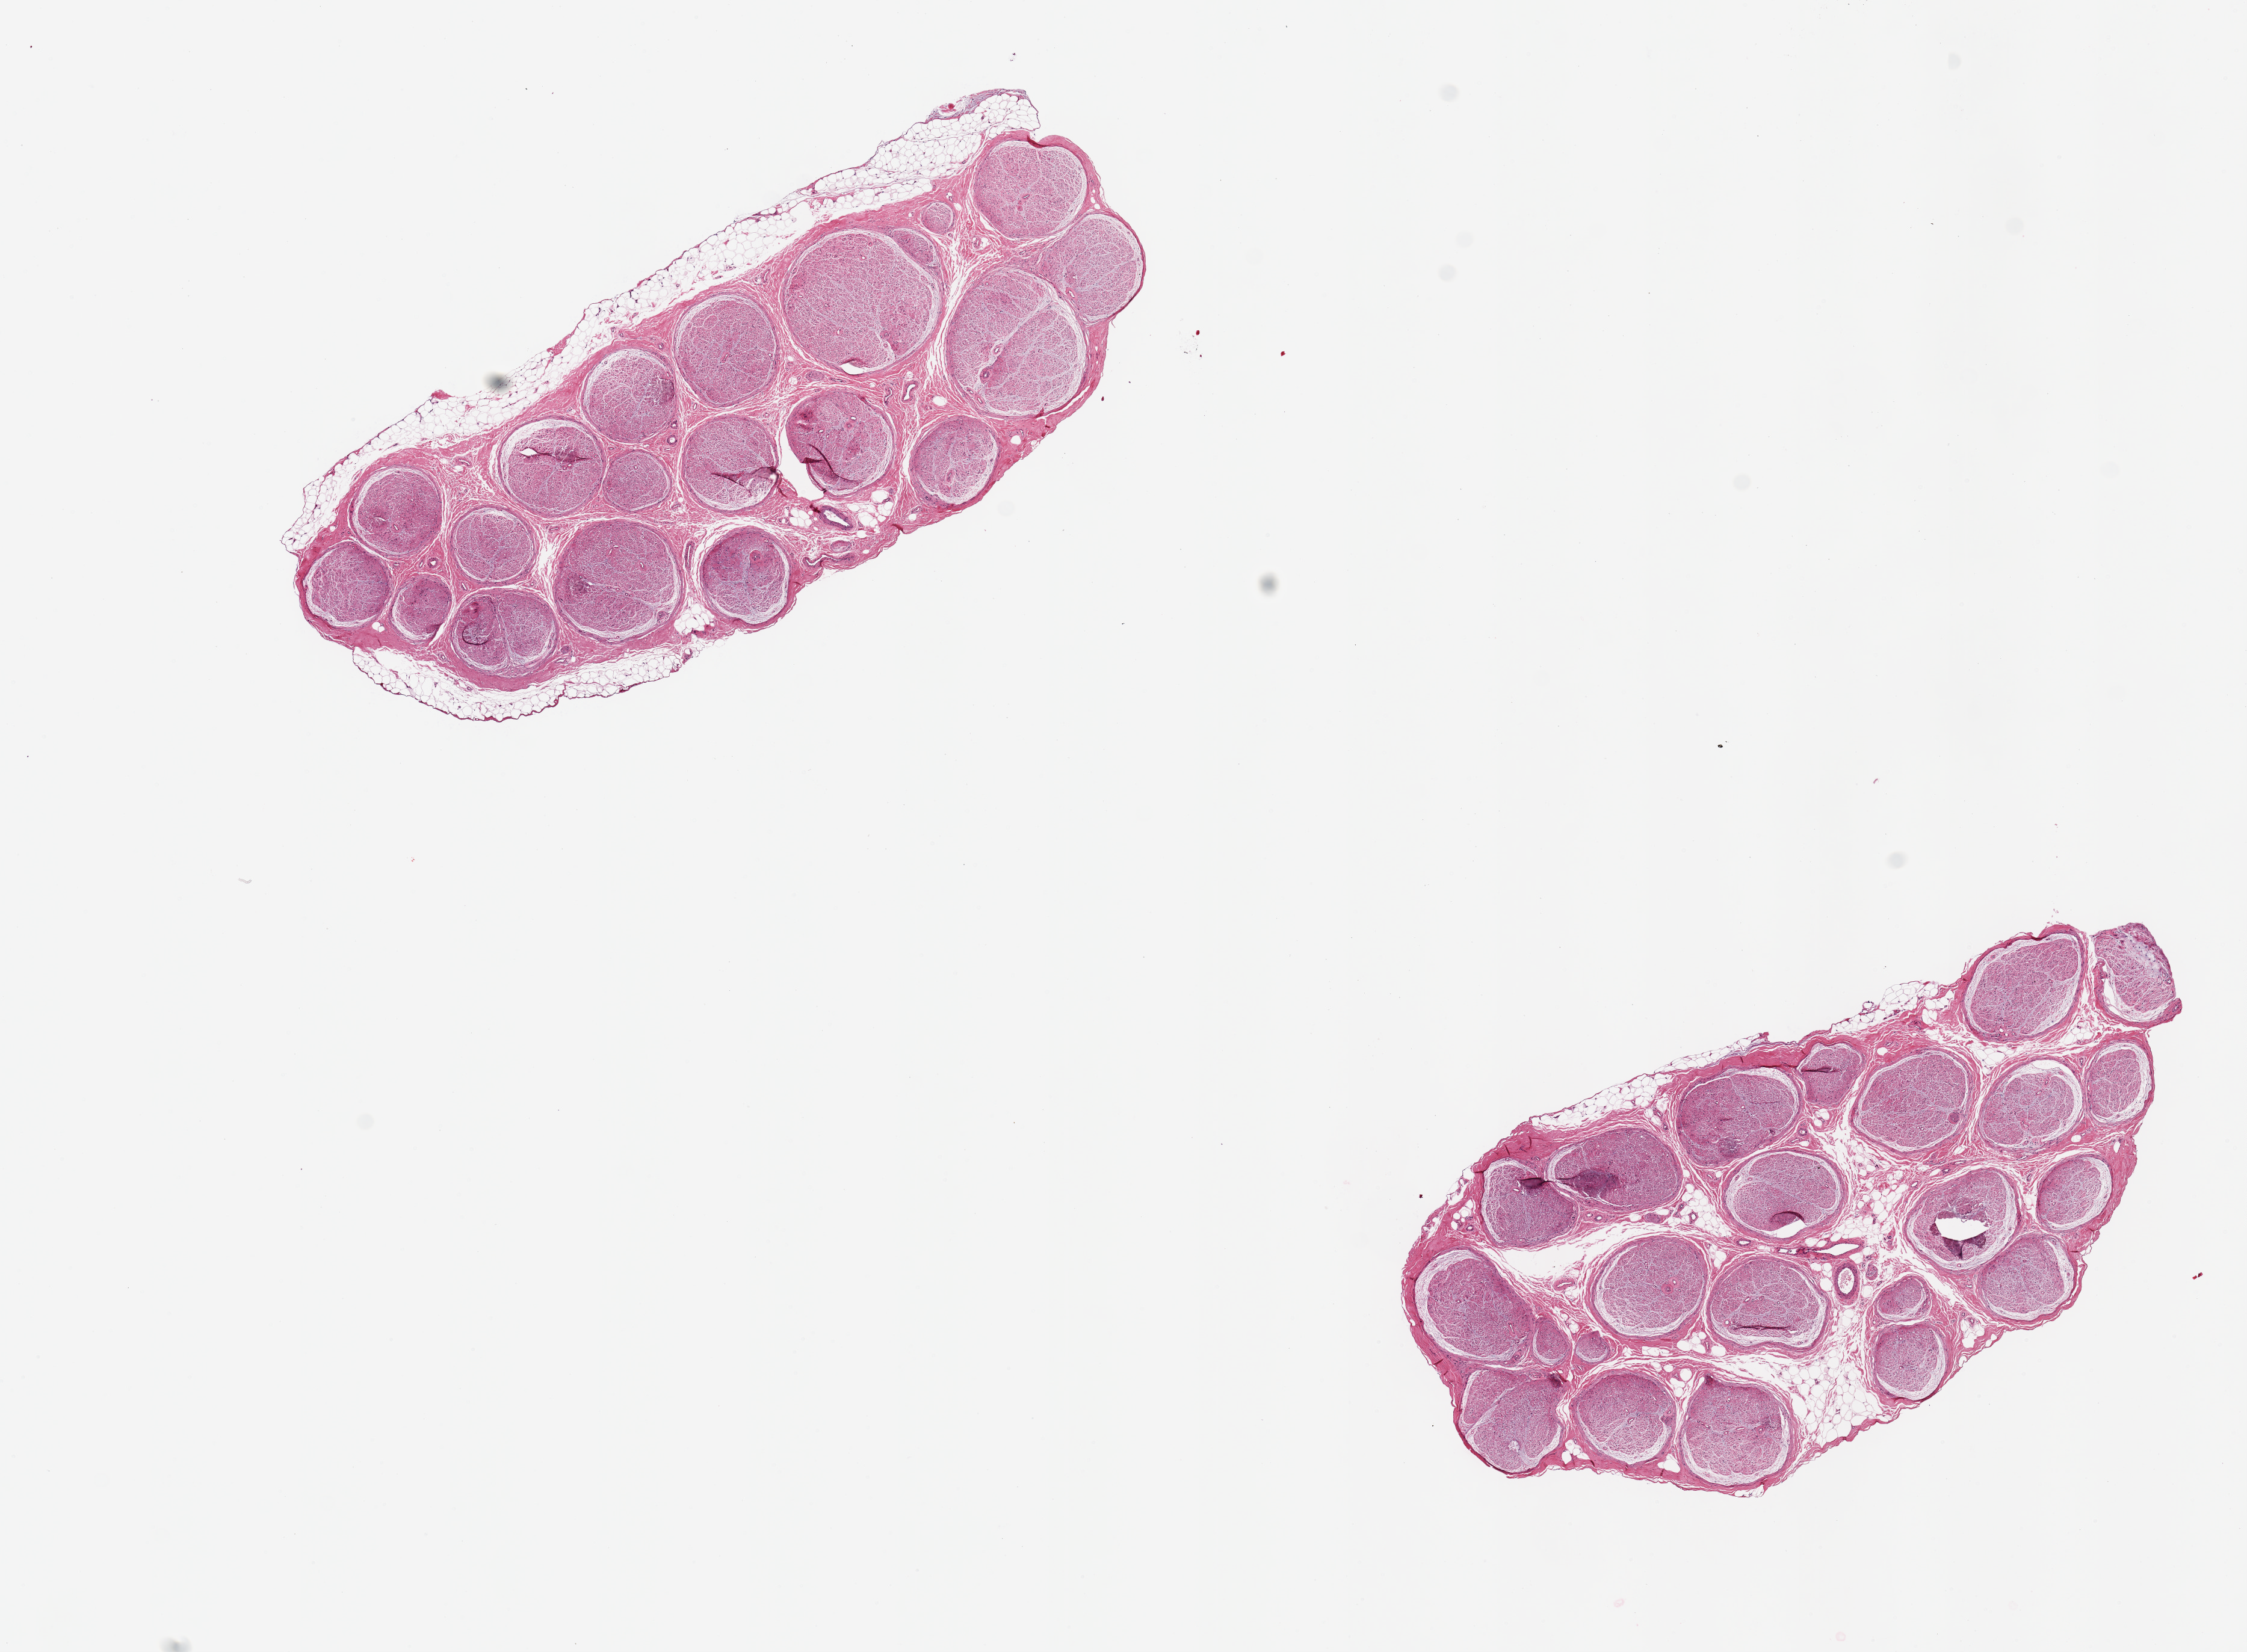
Haematoxylin and eosin whole-slide image, brightfield, low-resolution overview of the scanned area, about 14.8 x 10.9 mm; PAXgene-fixed paraffin-embedded (PFPE) section; section of tibial nerve (target tissue); donor tissue sample. Male donor.
Reviewer comment on this tissue sample: 2 pieces, 6x2 & 5.5x3mm; minimal adherent discontinuous fat on one ~0.5mm.